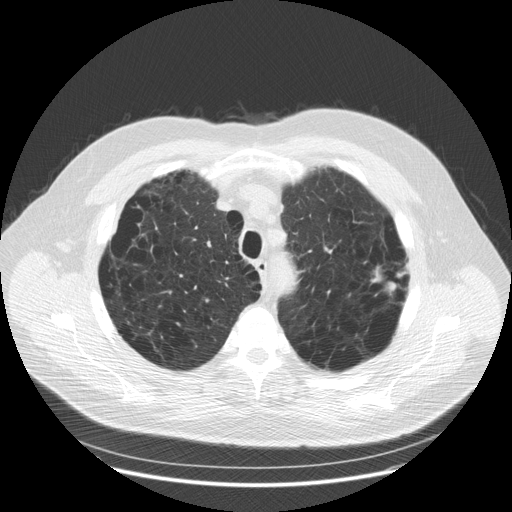
Low-dose screening chest CT, one axial slice. Slice 140 of 179 in the series (ordered by position). Reconstruction kernel STANDARD. Lung window (W 1500 / L -600 HU). 512 × 512 image matrix, field of view 404 × 404 mm.
Outlined on this slice (manually delineated by an expert):
- lesion 1 (tumor, upper lobe of left lung): bounding box <371,266,404,295> (left, top, right, bottom; pixels)